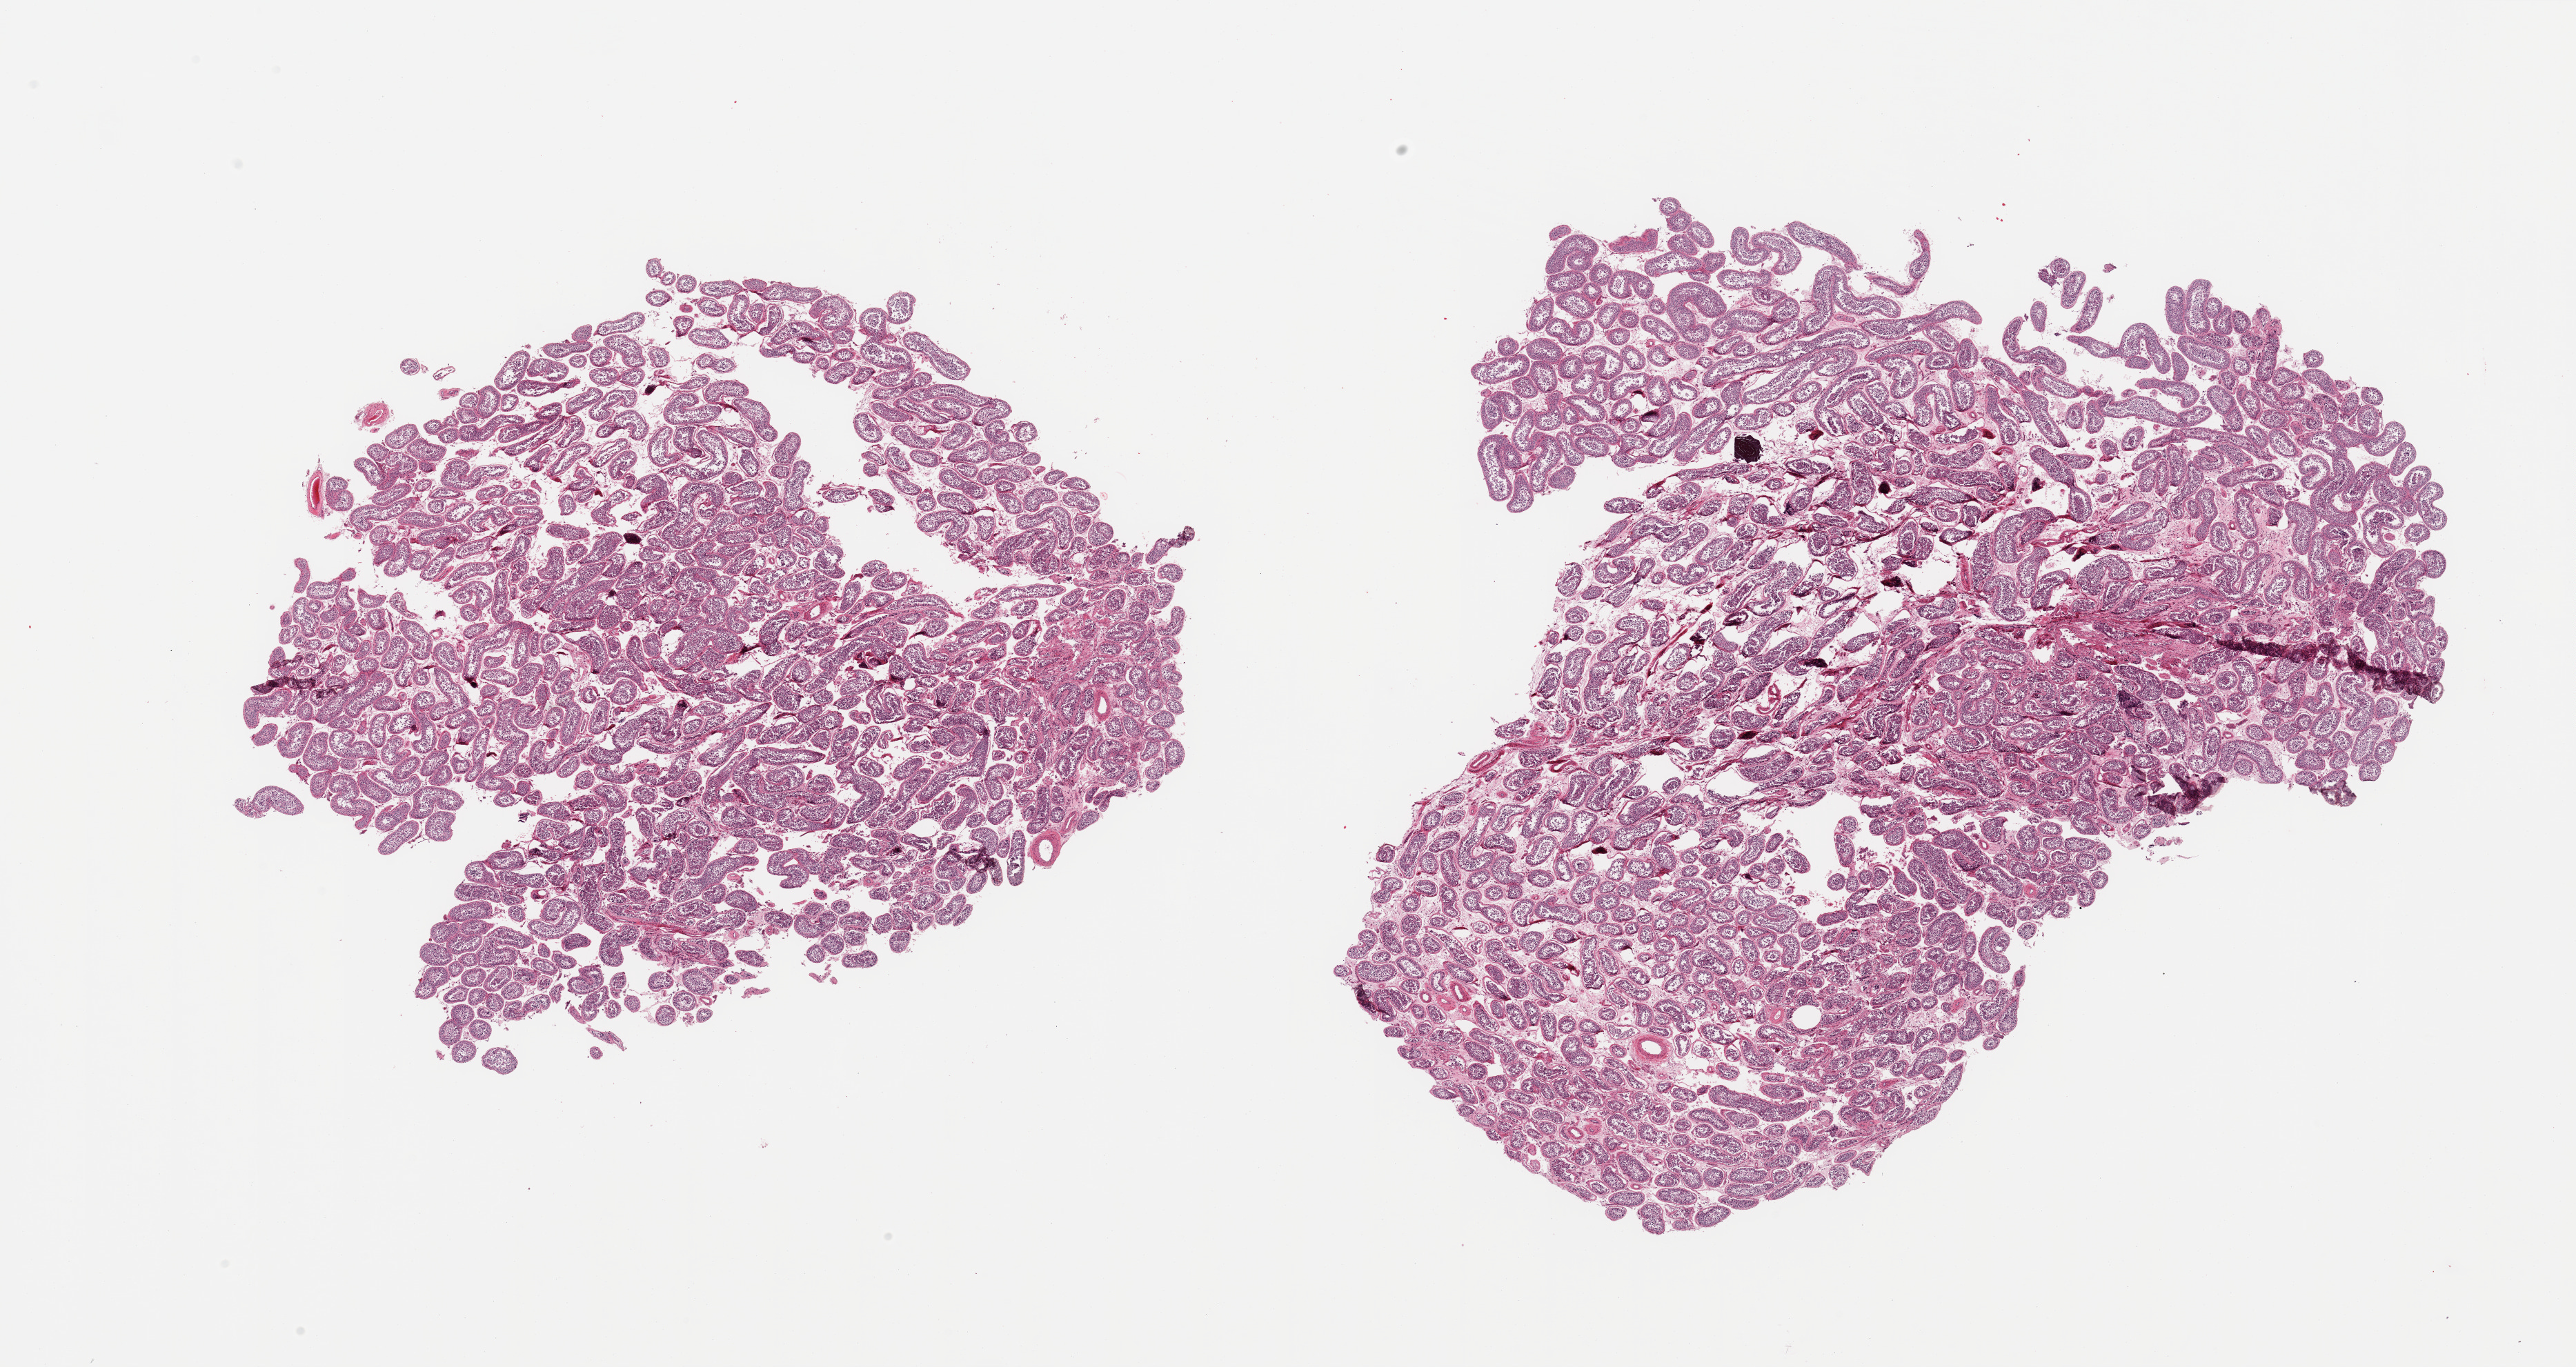
Hematoxylin and eosin (H&E) whole-slide image, a low-resolution overview of the entire scanned area, about 29.5 x 15.7 mm (acquisition: 20x scan), PAXgene-fixed, paraffin-embedded tissue, target tissue: testis, tissue donor sample. Donor sex: male.
Review note (as recorded): 2 pieces; spermatogenesis present.